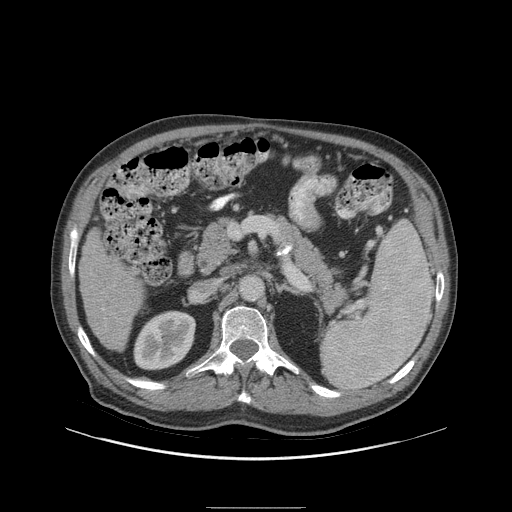
Contrast-enhanced abdominal CT (liver protocol), one axial slice; slice 39 of 105 in the series (ordered by position); reconstruction kernel STANDARD; soft-tissue window (W 400 / L 40 HU); 2.5 mm slice thickness; 512 × 512 image matrix, field of view 440 × 440 mm. From the clinical record (not read from this slice): diagnosis: hepatocellular carcinoma (patient treated with transarterial chemoembolisation; whether this scan precedes or follows treatment is not stated here); TNM stage (as recorded): Stage-I; Child-Pugh class: A.
Structures marked on this image (semi-automatically segmented with operator editing):
- liver parenchyma outside the tumour (the mass and vessels are separate outlines, so this box may not span the whole liver): bounding box [x1, y1, x2, y2] px = [78, 228, 144, 350]